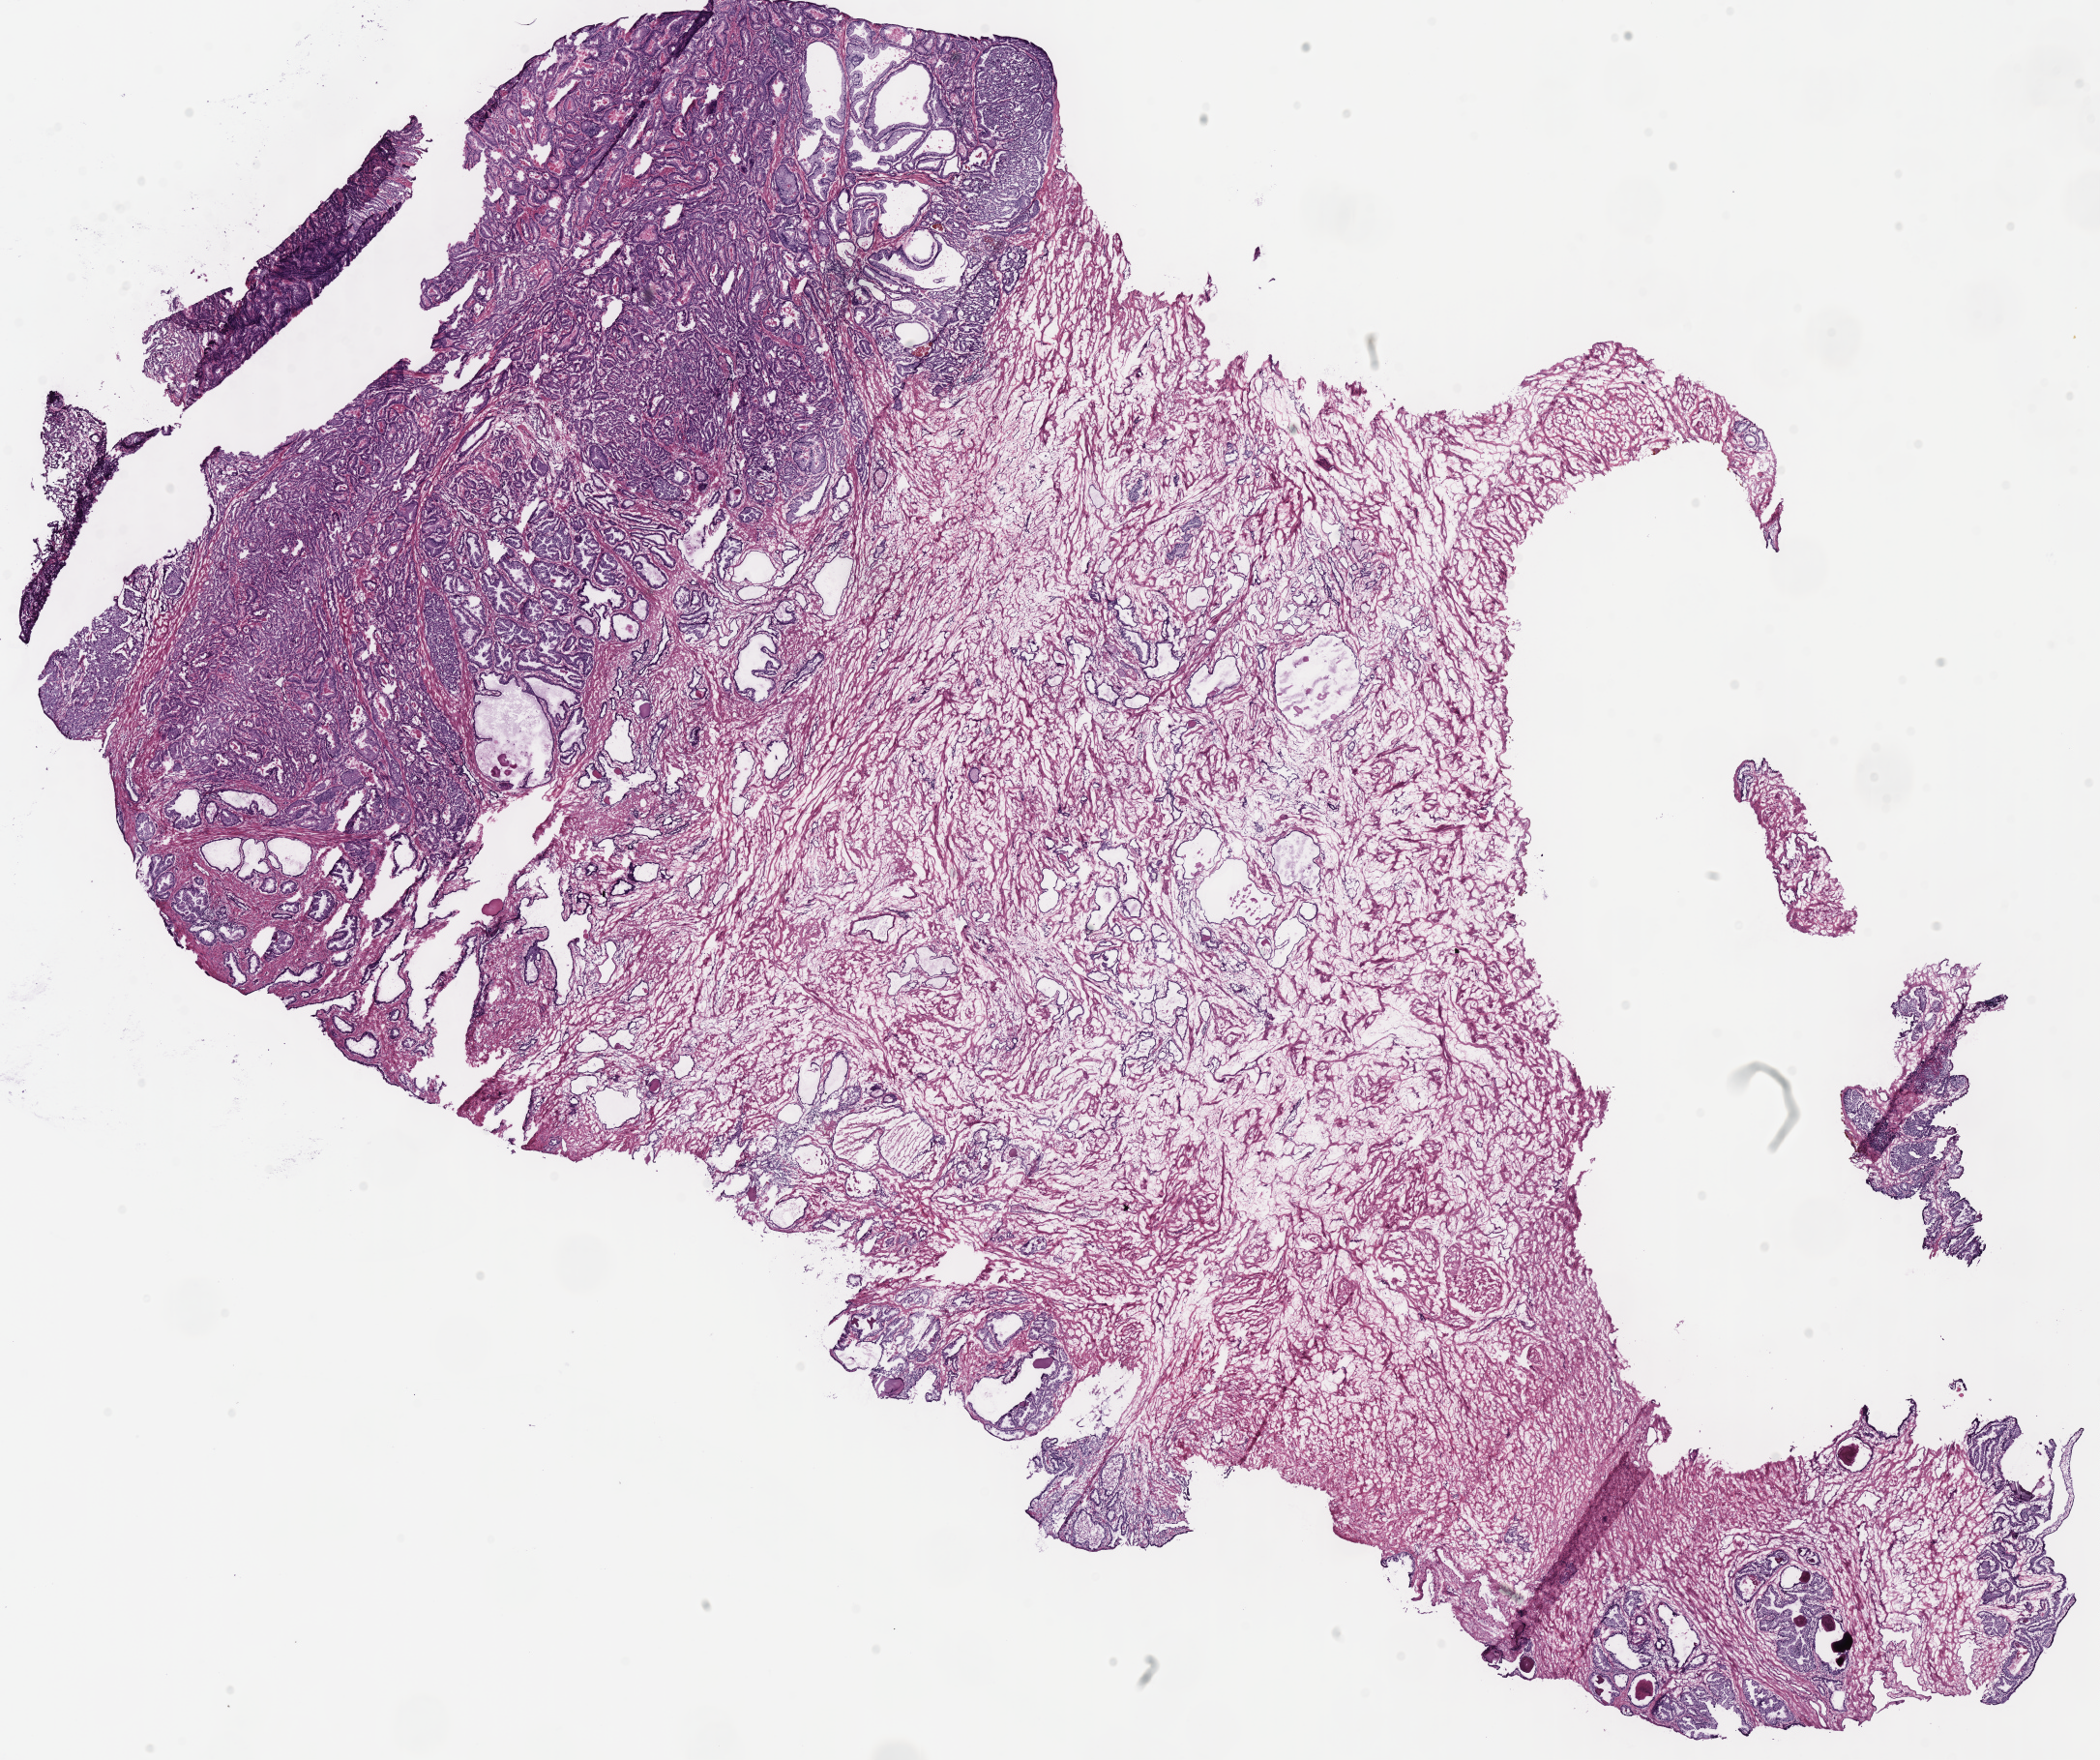
Digitized Hematoxylin and eosin (H&E) stained tissue section (whole slide), whole scanned area (about 17.1 x 14.3 mm) shown as a low-resolution overview; frozen section from the bottom of the tissue portion; sample: primary tumour, prostate. Male patient; age at initial diagnosis 64 years. Gleason score: 7 (3+4). Composition of this section per pathologist review: tumour cells 65%, tumour nuclei 60%, normal cells 15%, stromal cells 20%, necrosis 0%. Infiltration values recorded for this section: lymphocyte infiltration 2%, monocyte infiltration 0%, neutrophil infiltration 0%.
Pathologic diagnosis: Acinar cell carcinoma (prostate gland). Laterality: bilateral.